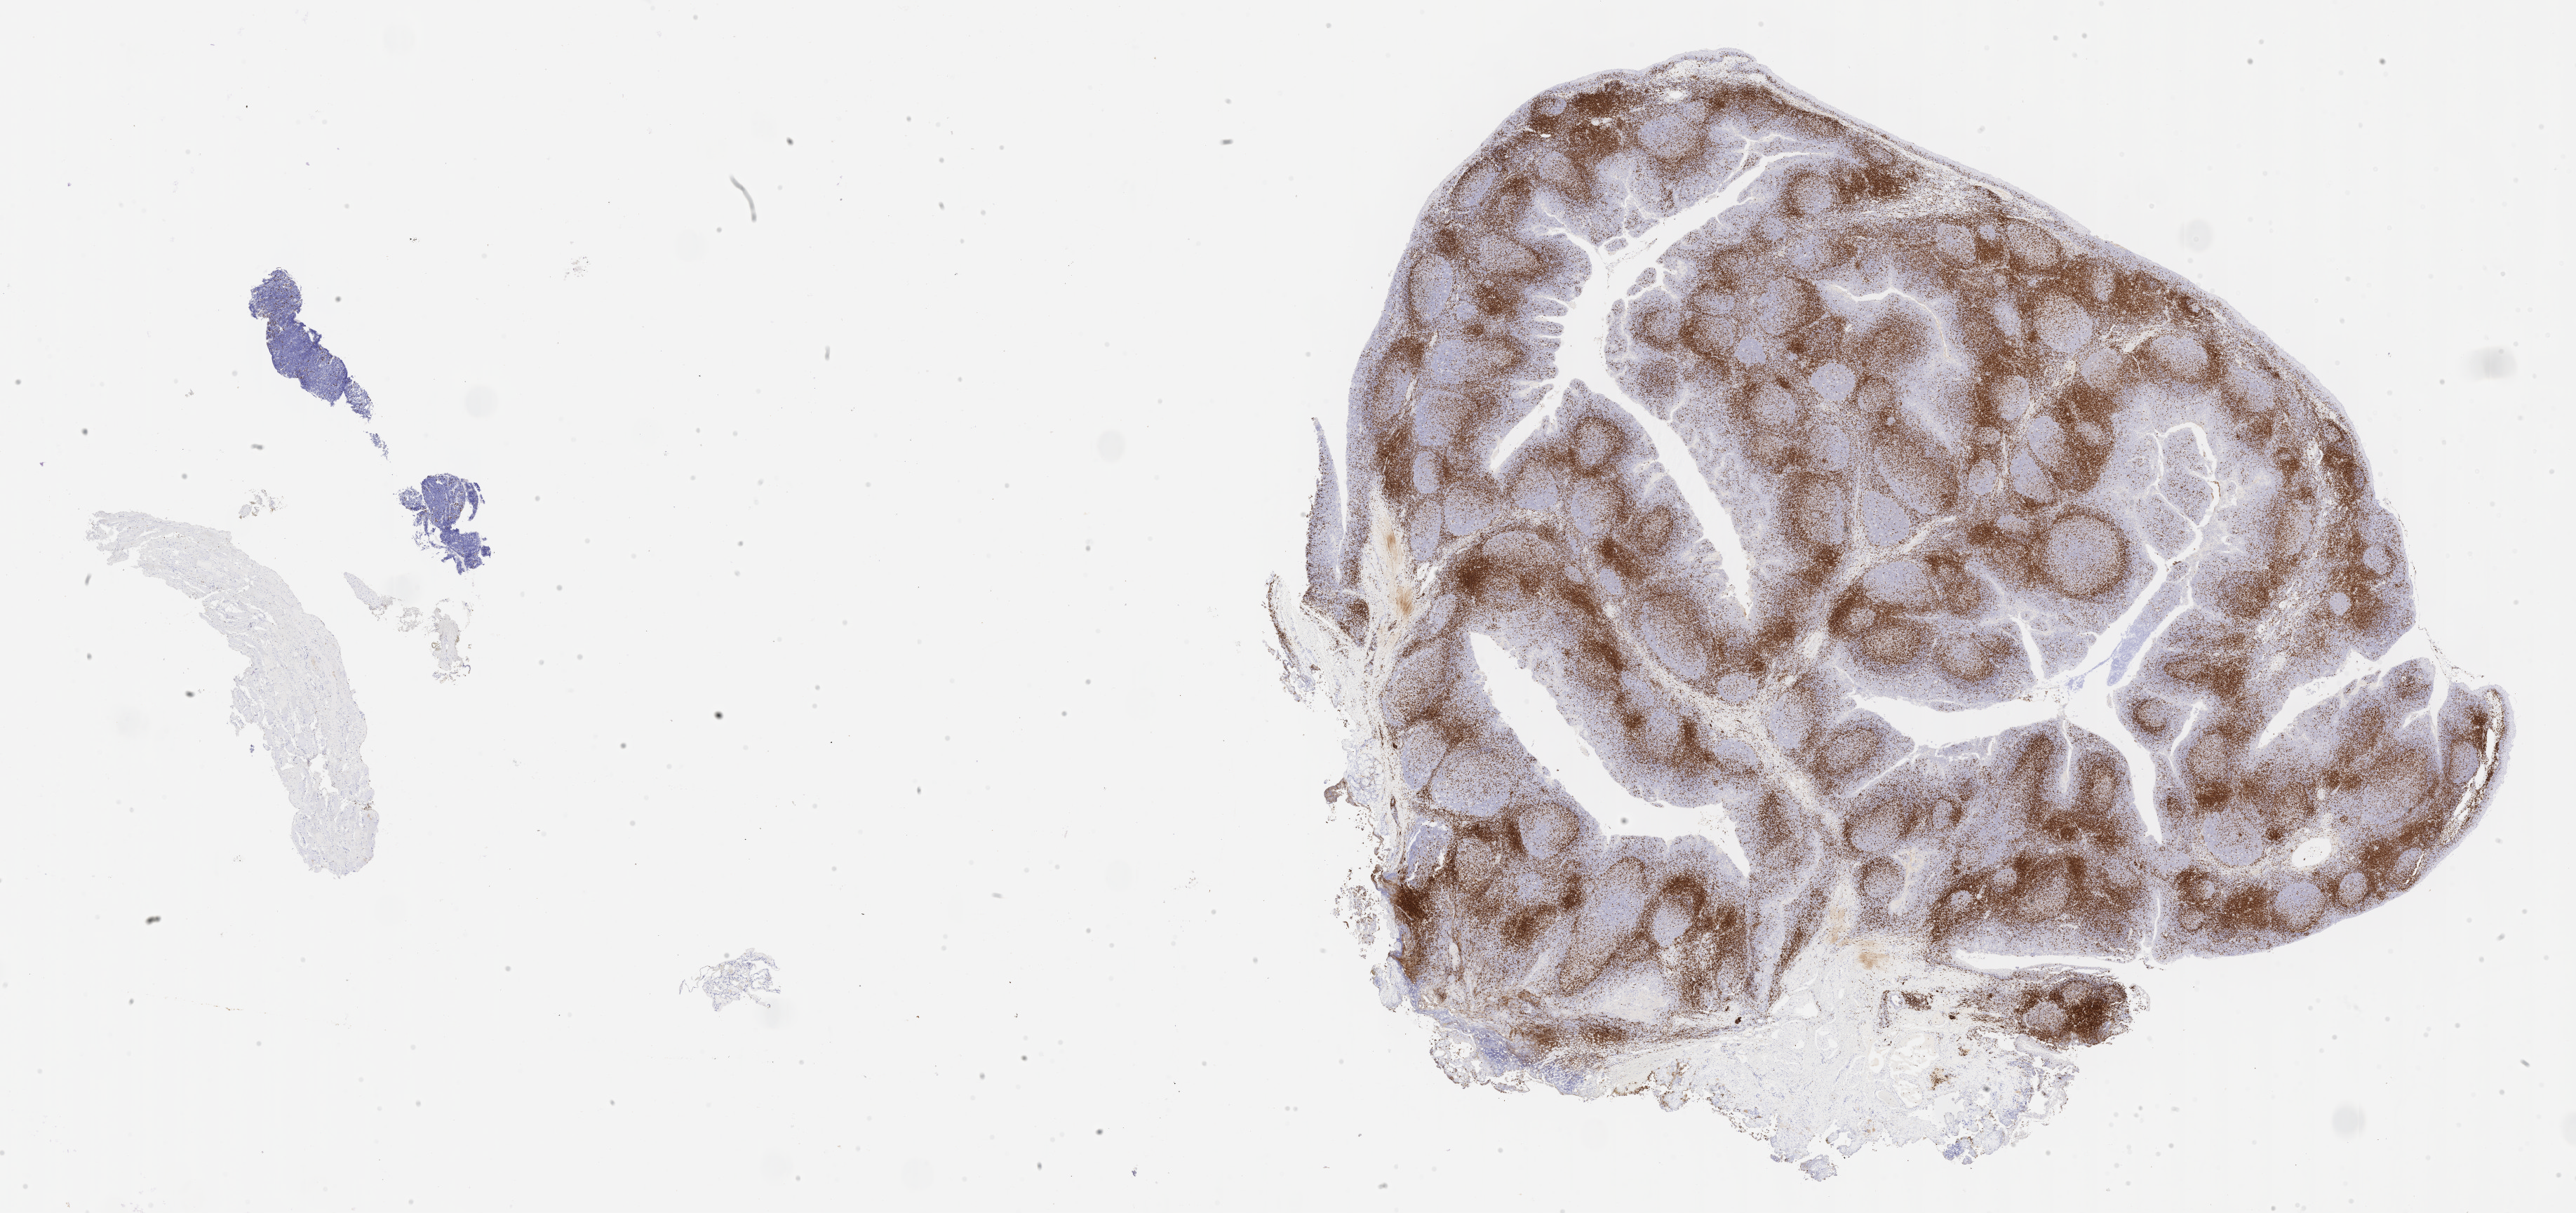
Whole-slide image, immunohistochemical stain for CD3 — whole scanned area (about 29.7 x 14.0 mm) shown as a low-resolution overview, specimen: tumor tissue, anatomic site: liver. Male patient.
Histologic diagnosis: Burkitt lymphoma, NOS.